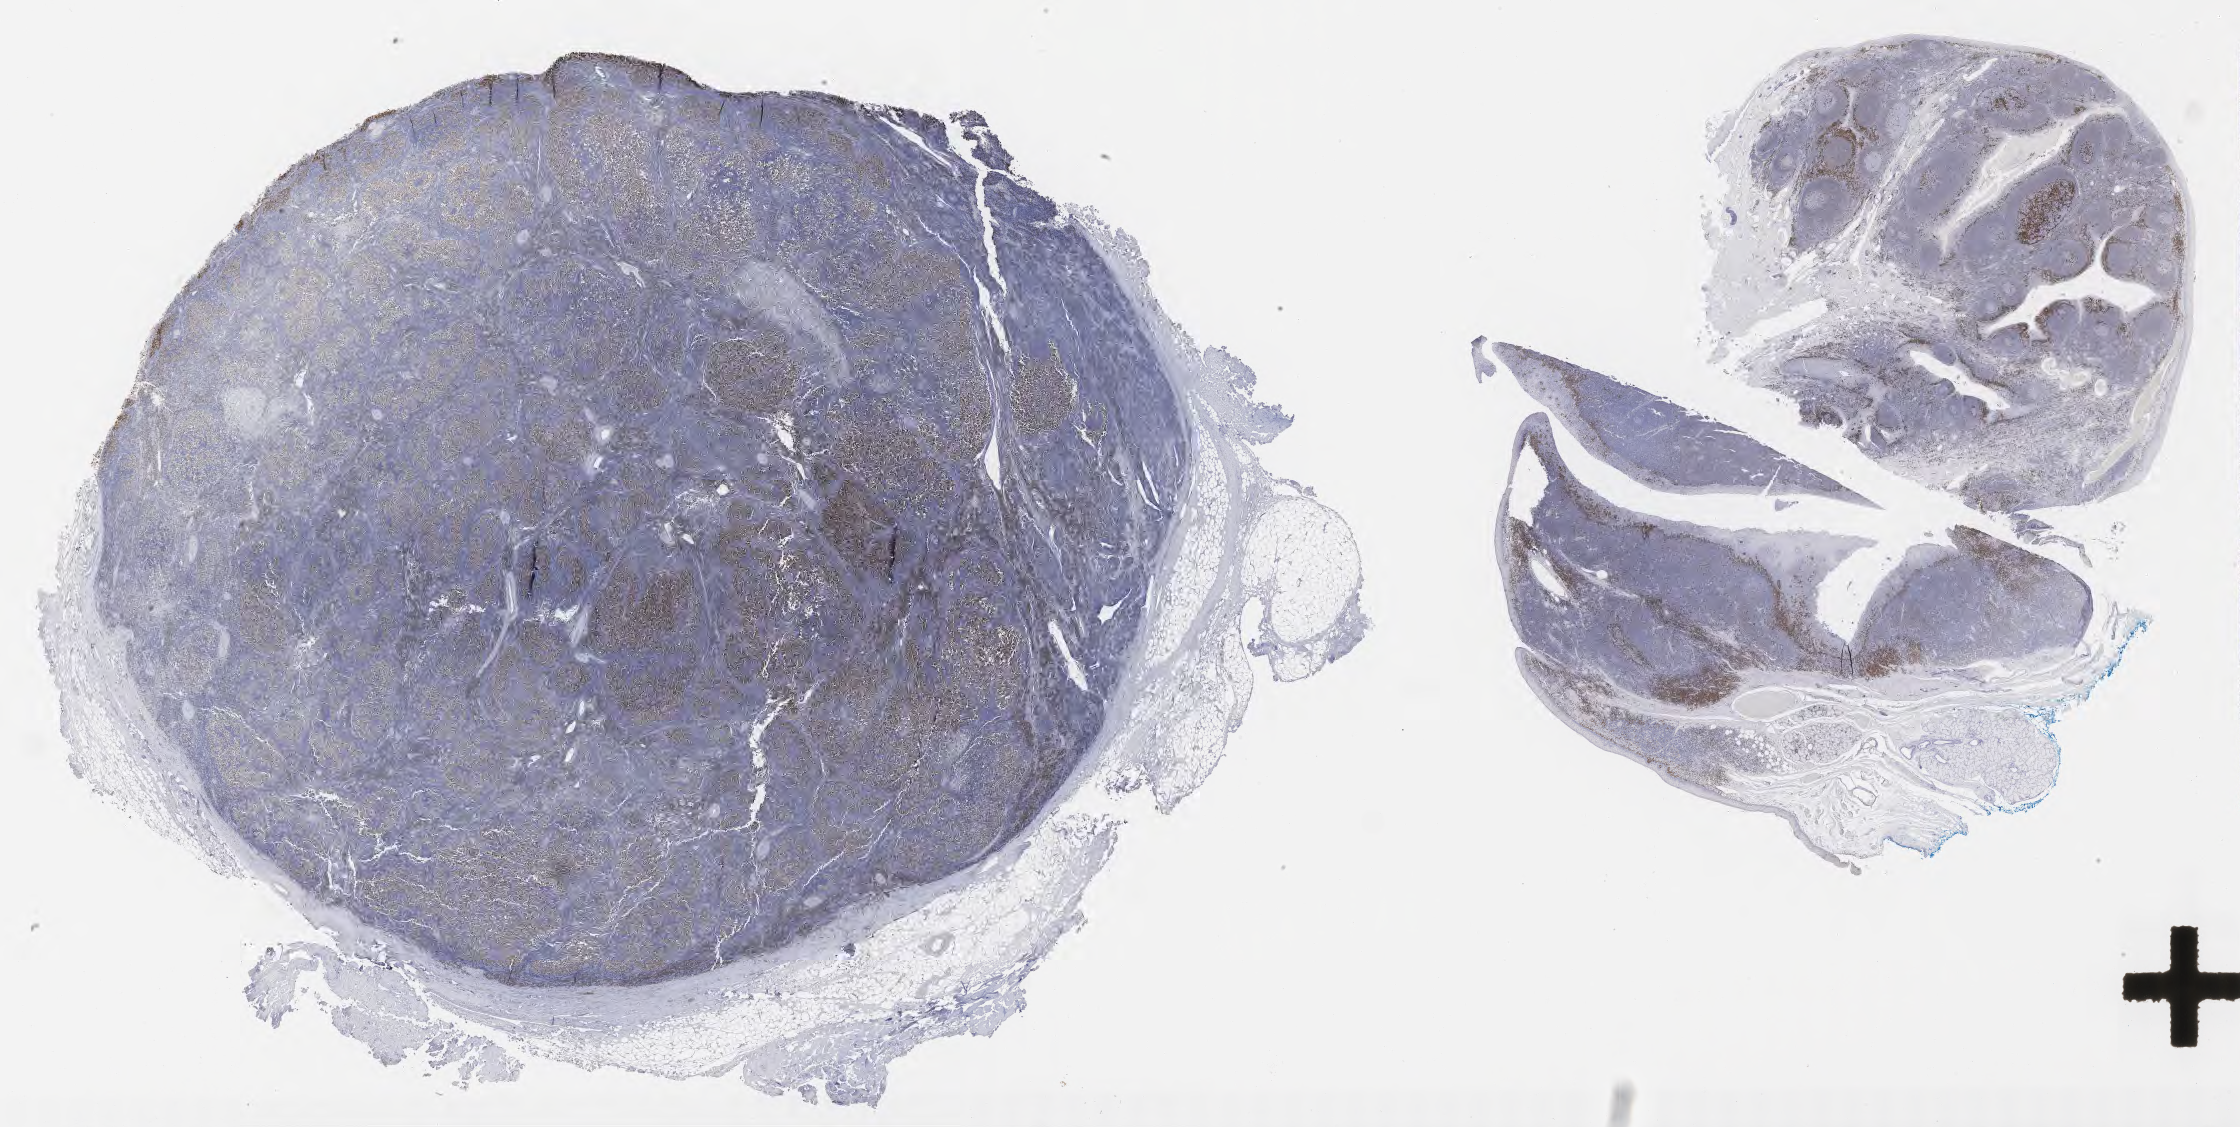
Whole-slide image, immunohistochemical stain for IRF4/MUM1, whole scanned area (about 36.2 x 18.2 mm) shown as a low-resolution overview; tumor tissue; anatomic site: lymph node. Patient male; age 46 years.
Histologic diagnosis: Diffuse large B-cell lymphoma, NOS.